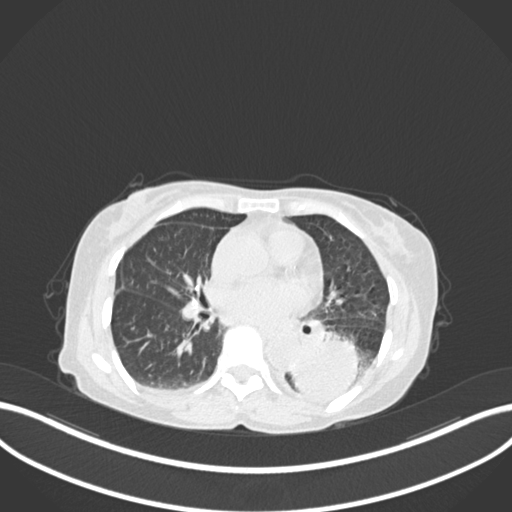
Chest CT, one axial slice; slice 73 of 233 in the series (ordered by position); reconstruction kernel B30f; 120 kVp; lung window (W 1500 / L -600 HU); 1 mm slice thickness; 512 × 512 image matrix. Patient: female, 78 years. Case-level facts recorded for this patient, not image findings: clinical TNM (as recorded): T3 N0 M1.
Structures marked on this image (rectangle marked by the reading radiologist):
- lung tumour (recorded histology: squamous cell carcinoma): bounding box <288,328,360,404> (left, top, right, bottom; pixels)